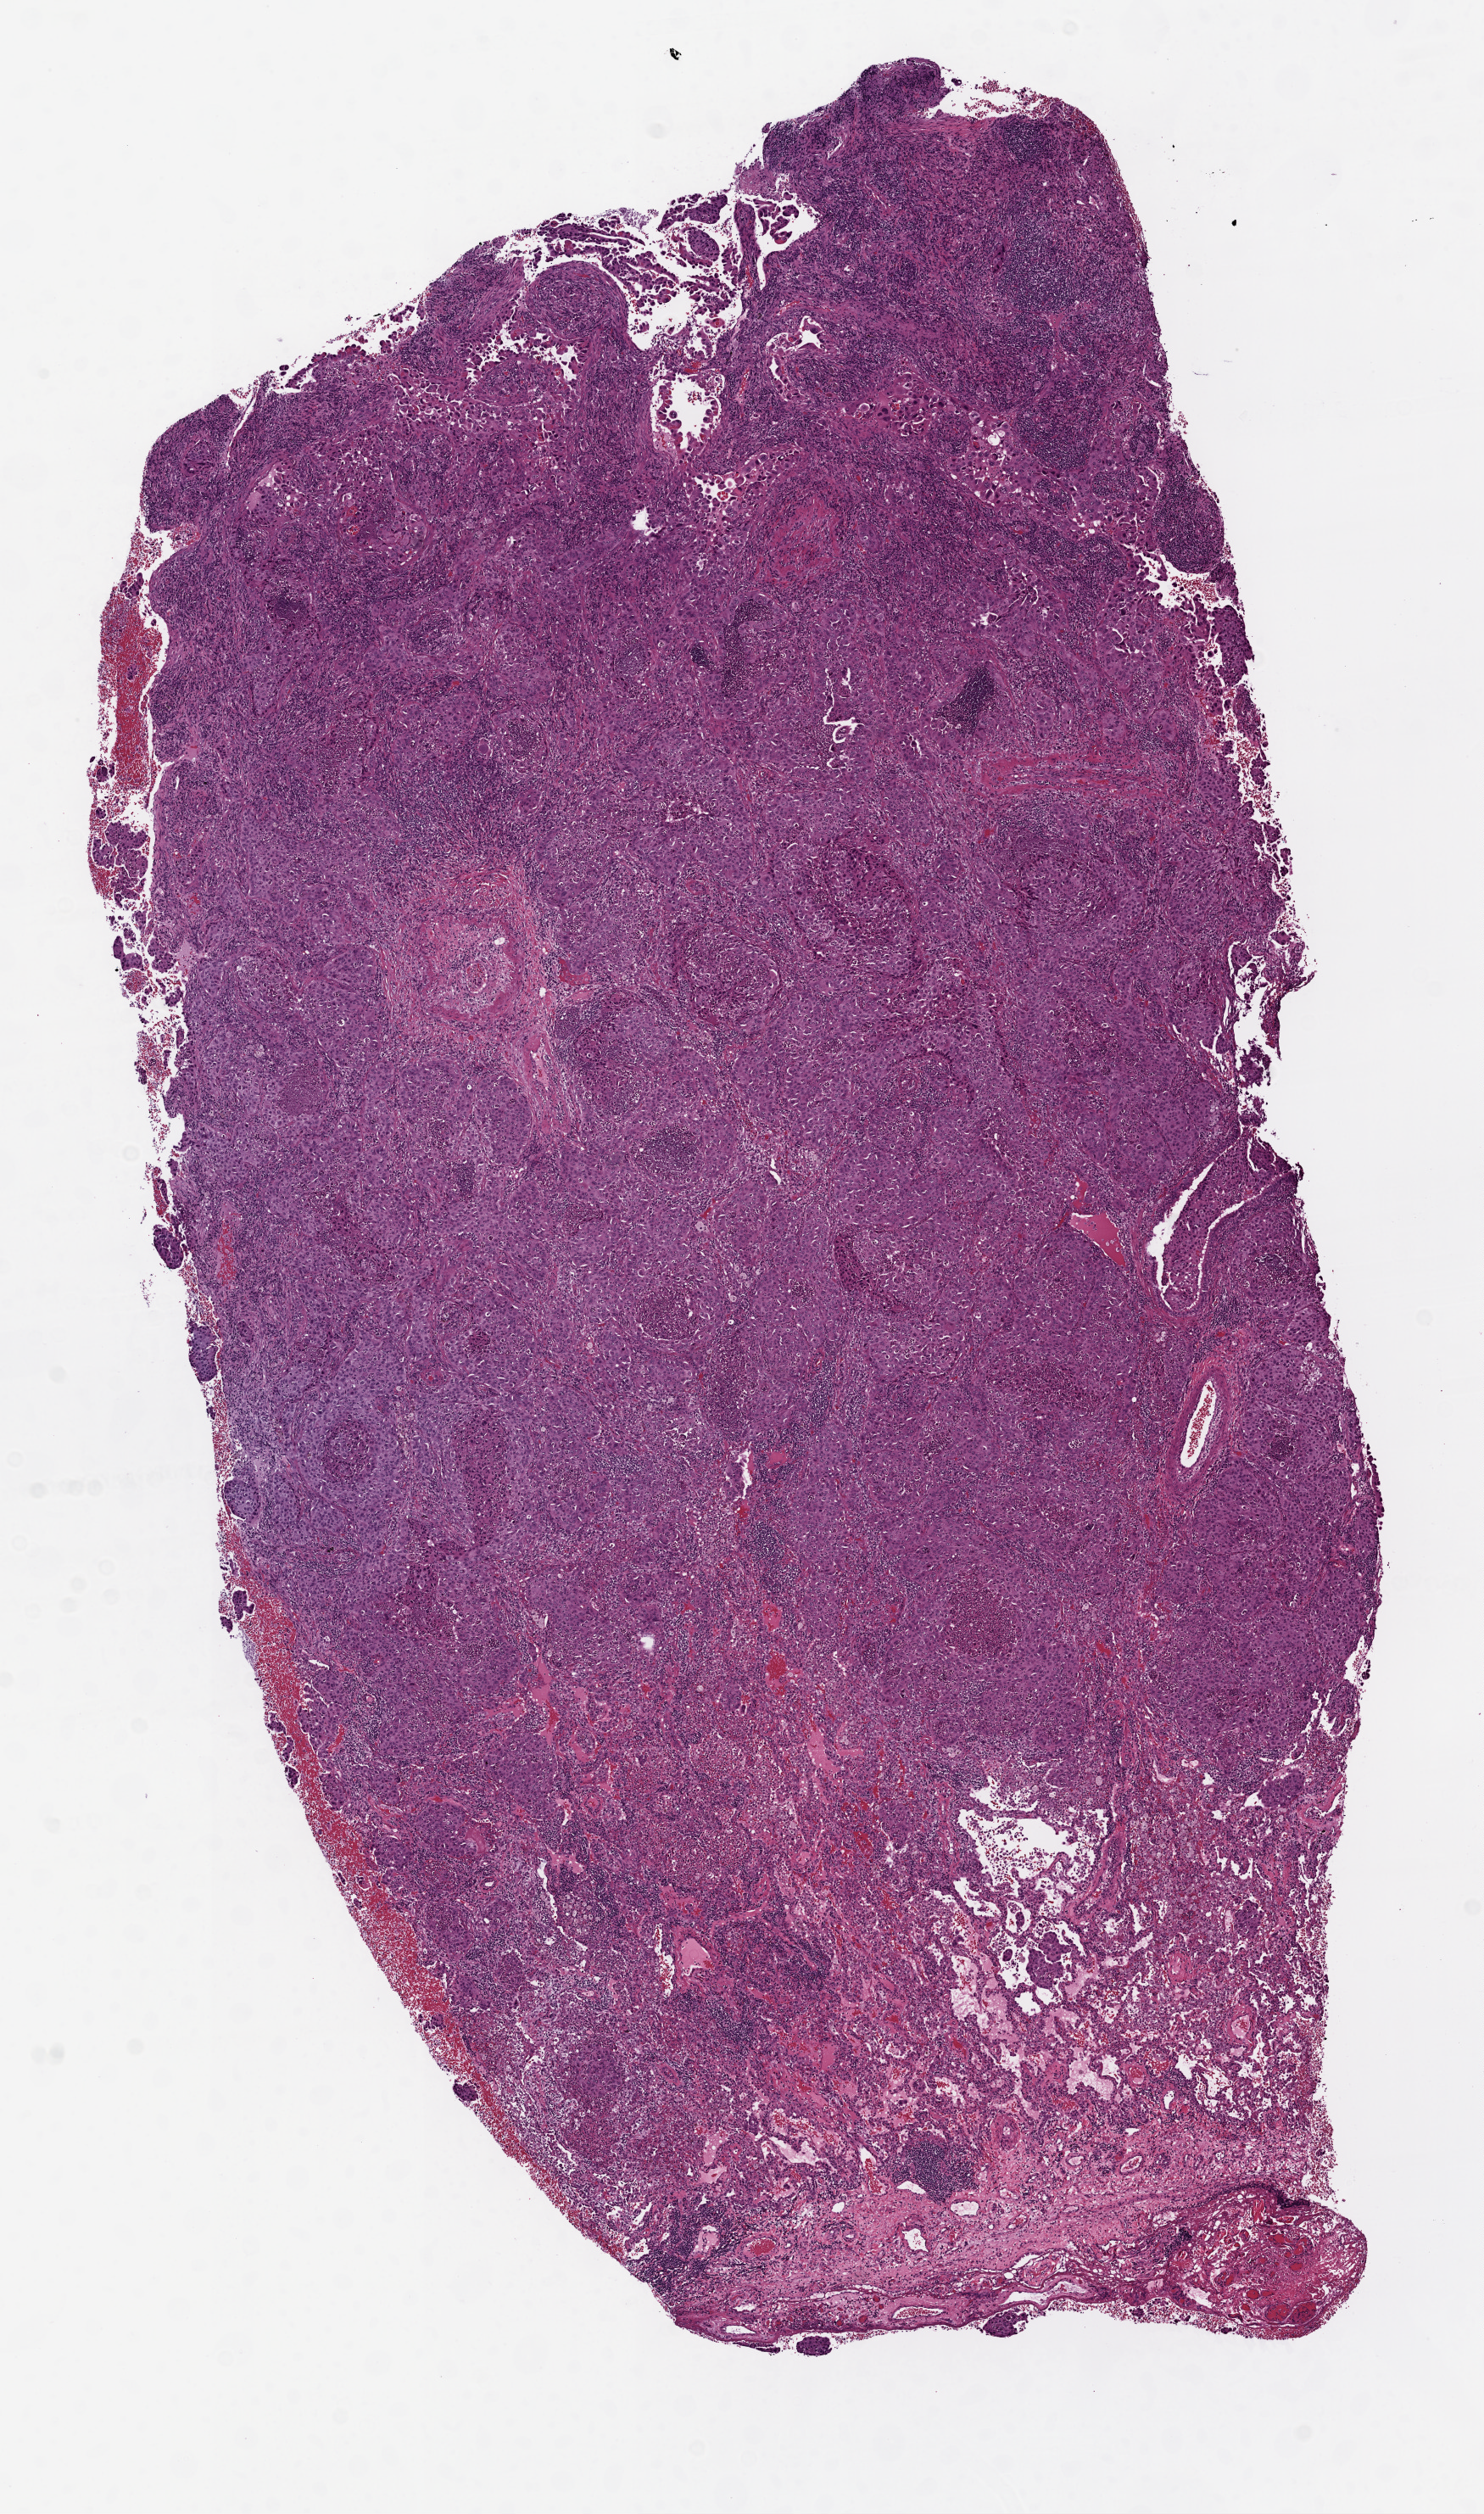
H&E whole-slide image — low-resolution overview of the scanned area, about 7.0 x 11.9 mm (from a 20x scan); frozen section; primary tumour sample from the lung. Female, age 74 years at initial diagnosis. Slide review estimates, as recorded: tumour cells 75%, tumour nuclei 60%, normal cells 15%, stromal cells 5%, necrosis 5%. Infiltration values recorded for this section: lymphocyte infiltration 30%.
- diagnosis: Adenocarcinoma, NOS (upper lobe, lung)
- AJCC pathologic stage: IIIA (7th edition)